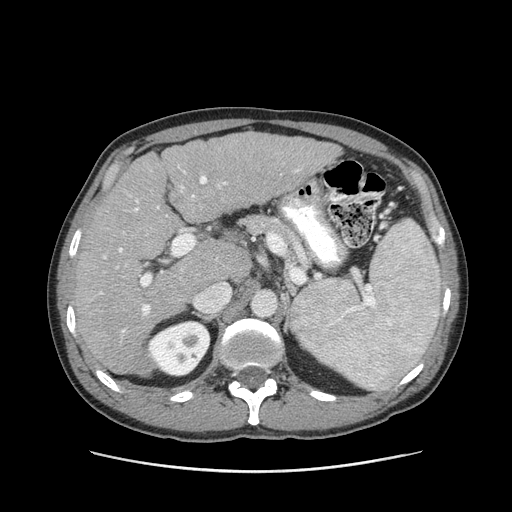
Contrast-enhanced abdominal CT (liver protocol), one axial slice; slice 57 of 93 in the series (ordered by position); 120 kVp; soft-tissue window (W 400 / L 40 HU); 512 × 512 image matrix, field of view 380 × 380 mm. From the clinical record (not read from this slice): diagnosis: hepatocellular carcinoma (patient treated with transarterial chemoembolisation; whether this scan precedes or follows treatment is not stated here); TNM stage (as recorded): Stage-II; Child-Pugh class: A; tumour differentiation: moderately differentiated; tumour size: 1 cm.
Annotated regions visible in this slice (semi-automatic segmentation, software-assisted and operator-edited):
- liver parenchyma outside the tumour (the mass and vessels are separate outlines, so this box may not span the whole liver): bounding box (x1, y1, x2, y2) in pixels: (74, 132, 340, 376)
- liver vessels: (99, 166, 300, 332)